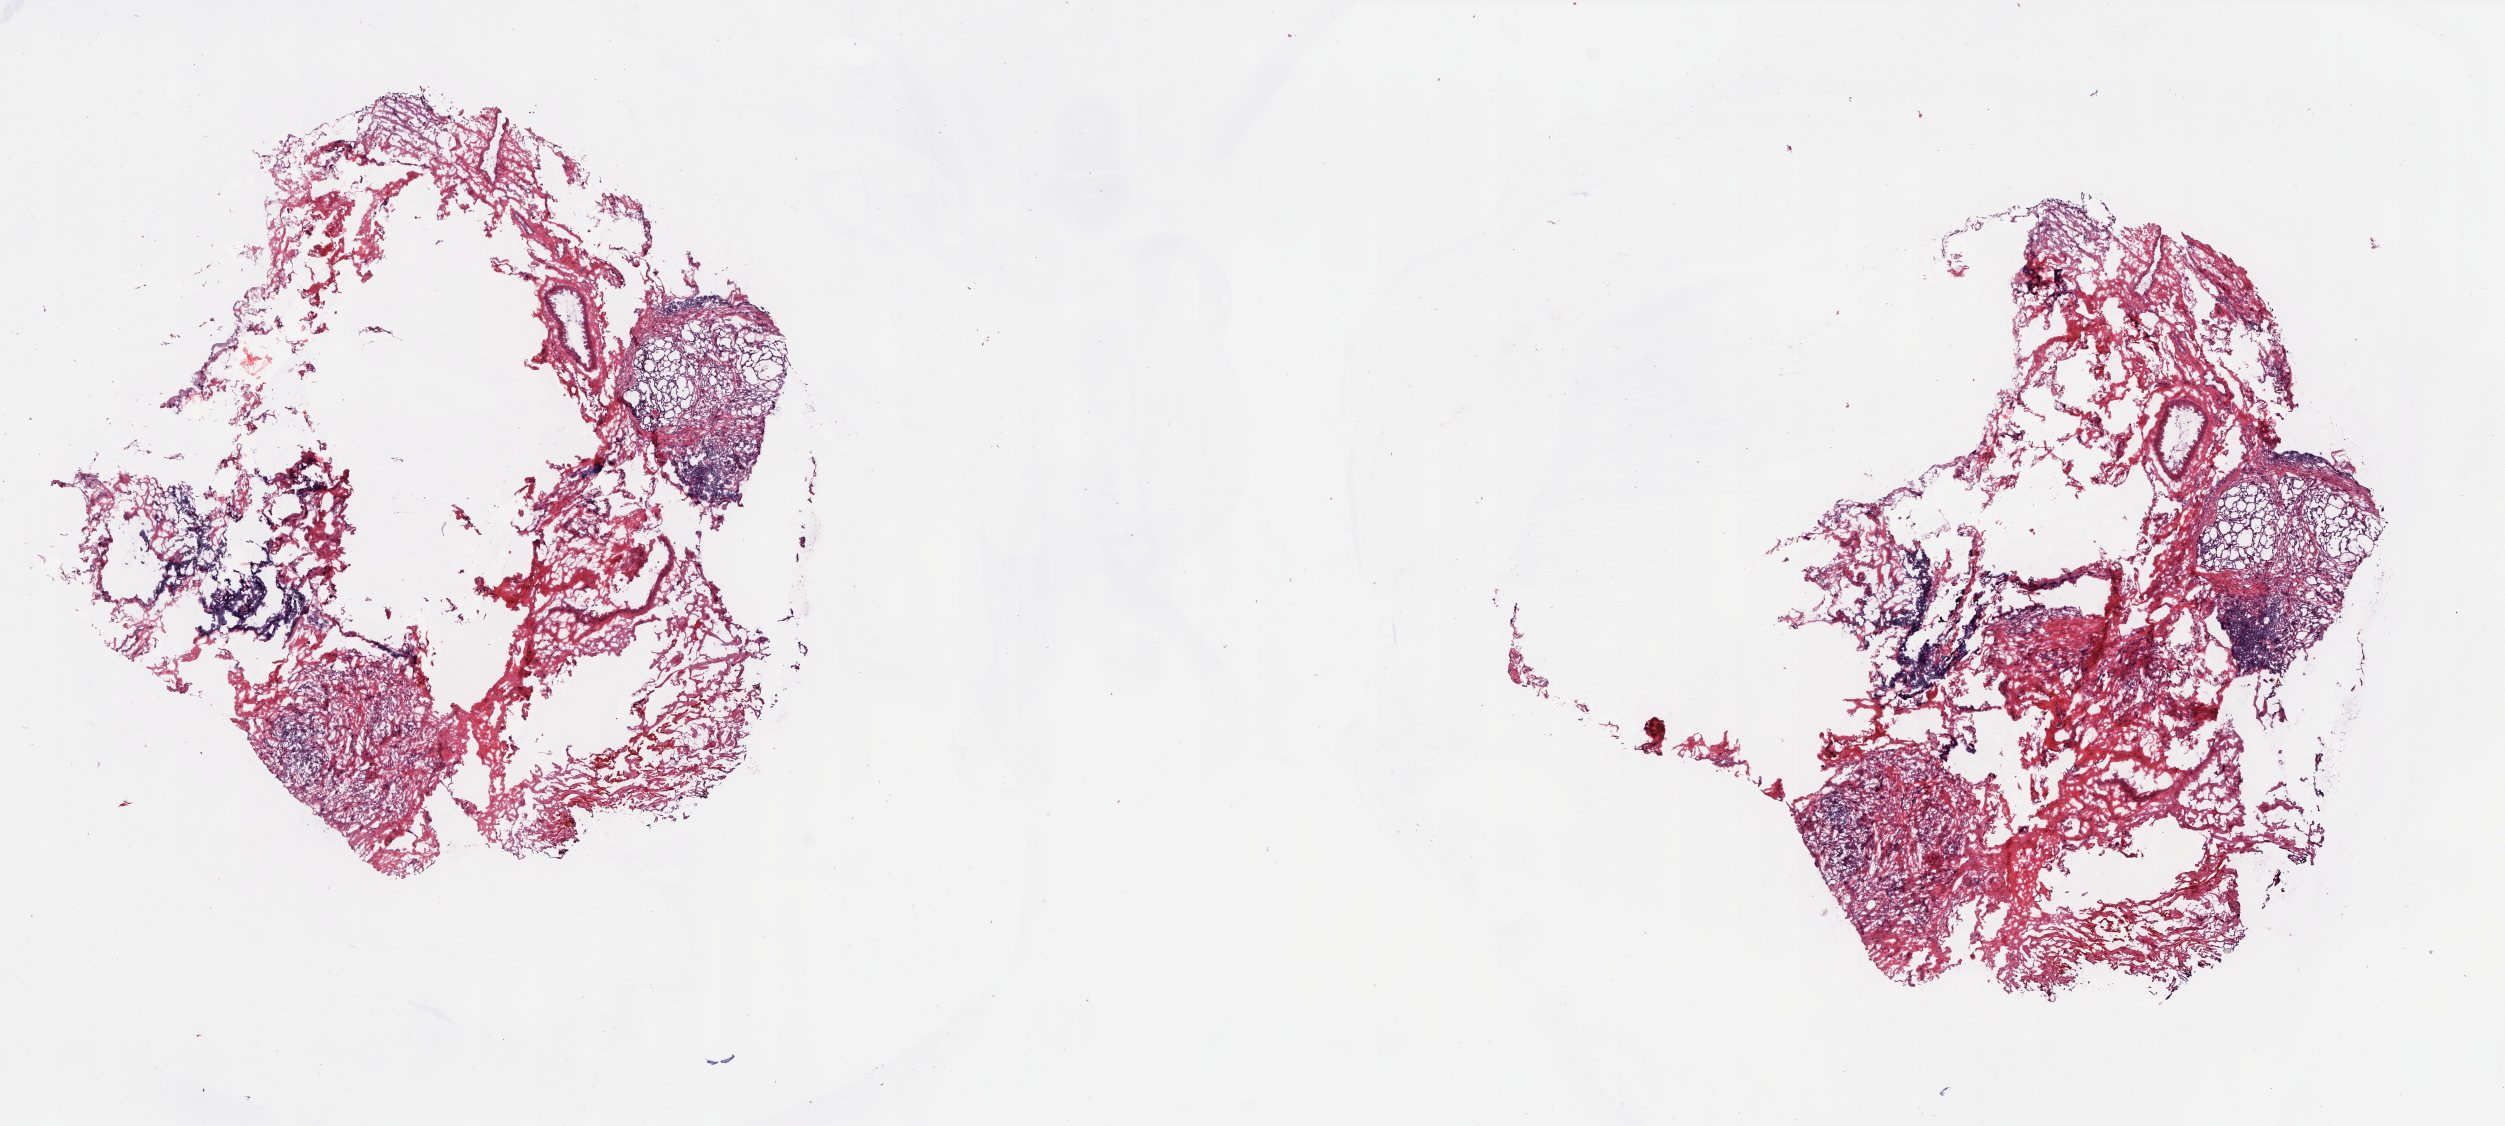
H&E whole-slide image, a low-resolution overview of the entire scanned area, about 20.2 x 9.1 mm (from a 20x scan), frozen section, solid tissue normal (non-tumour tissue) sample from the thyroid. Patient: female, age at initial diagnosis 55 years.
This section: solid tissue normal sample (biorepository sample class). Patient diagnosis: Papillary adenocarcinoma, NOS (thyroid gland).